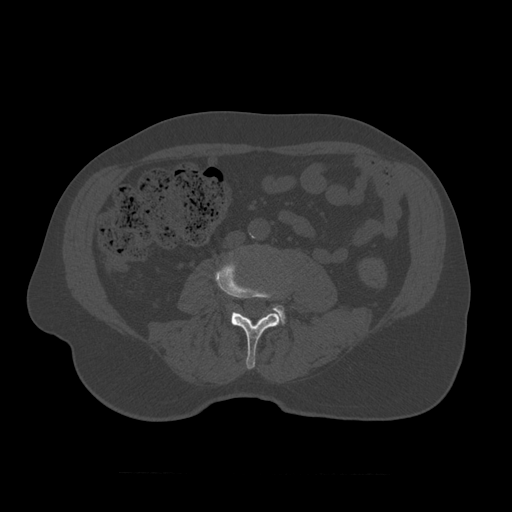
CT including the spine, one axial slice. Bone window (W 1800 / L 400 HU). 1.25 mm slice thickness. 512 × 512 image matrix, field of view 405 × 405 mm. Patient age 75 years. Case-level facts recorded for this patient, not image findings: primary cancer: prostate.
Structures marked on this image (semi-automatically segmented with operator editing):
- L3 vertebra: bounding box (x1, y1, x2, y2) in pixels: (215, 253, 282, 370)
- L4 vertebra: (230, 253, 286, 325)